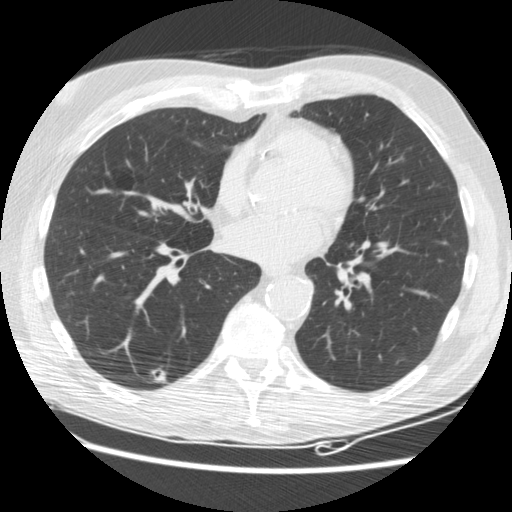
Chest CT (low-dose screening protocol), one axial image. Third annual screen. Lung window (W 1500 / L -600 HU). 2.5 mm slice thickness. Standard (soft-tissue) reconstruction kernel (STANDARD). Slice 98 of 176 in the series. 512 × 512 image matrix, field of view 347 × 347 mm. Male, age 62 years at enrolment.
• Expert-annotated lung lesion, bounding box (x1, y1, x2, y2) in pixels: (141, 358, 180, 395).
• The screening reader recorded 3 non-calcified nodules or masses ≥4 mm on this exam (right lower lobe, right lower lobe, right lower lobe); which of them this box marks is not recorded.
• Official screen result: positive, other.
• Participant outcome: lung cancer diagnosed 33 days after this screen — adenocarcinoma, NOS, right lower lobe, moderately differentiated (G2), stage IIIB (AJCC 6th edition), 15 mm at pathology.